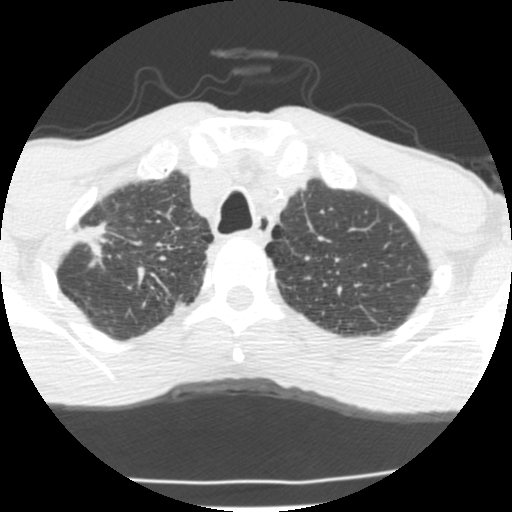
Low-dose screening chest CT, one axial slice; position 179 of 214 along the scan axis; 120 kVp; lung window (W 1500 / L -600 HU); 2.5 mm slice thickness; 512 × 512 image matrix, field of view 283 × 283 mm.
Annotated regions visible in this slice (outlined manually by an expert reader):
- lesion 1 (tumor, upper lobe of right lung): box from (x=73, y=221) to (x=108, y=267) px